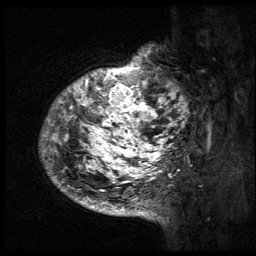
Breast MRI (dynamic contrast-enhanced), one sagittal slice. Slice 13 of 64 in the series (ordered by position). 3 images stored at this slice position (order not interpretable as contrast timing). 1.5 T. TE 4.2 ms, TR 9 ms. 256 × 256 image matrix, field of view 180 × 180 mm. Patient: female, 50 years. From the clinical record (not read from this slice): setting: breast cancer imaged before/during neoadjuvant chemotherapy; receptor status: triple-negative.
Structures marked on this image (semi-automatically segmented with operator editing):
- analysis volume of interest (the breast-tissue region the enhancement analysis was run in; not a lesion): bounding box (x1, y1, x2, y2) in pixels: (39, 39, 194, 212)
- tumour enhancement mask (voxels above the 140 % enhancement threshold inside the analysis volume of interest): (40, 48, 191, 212)